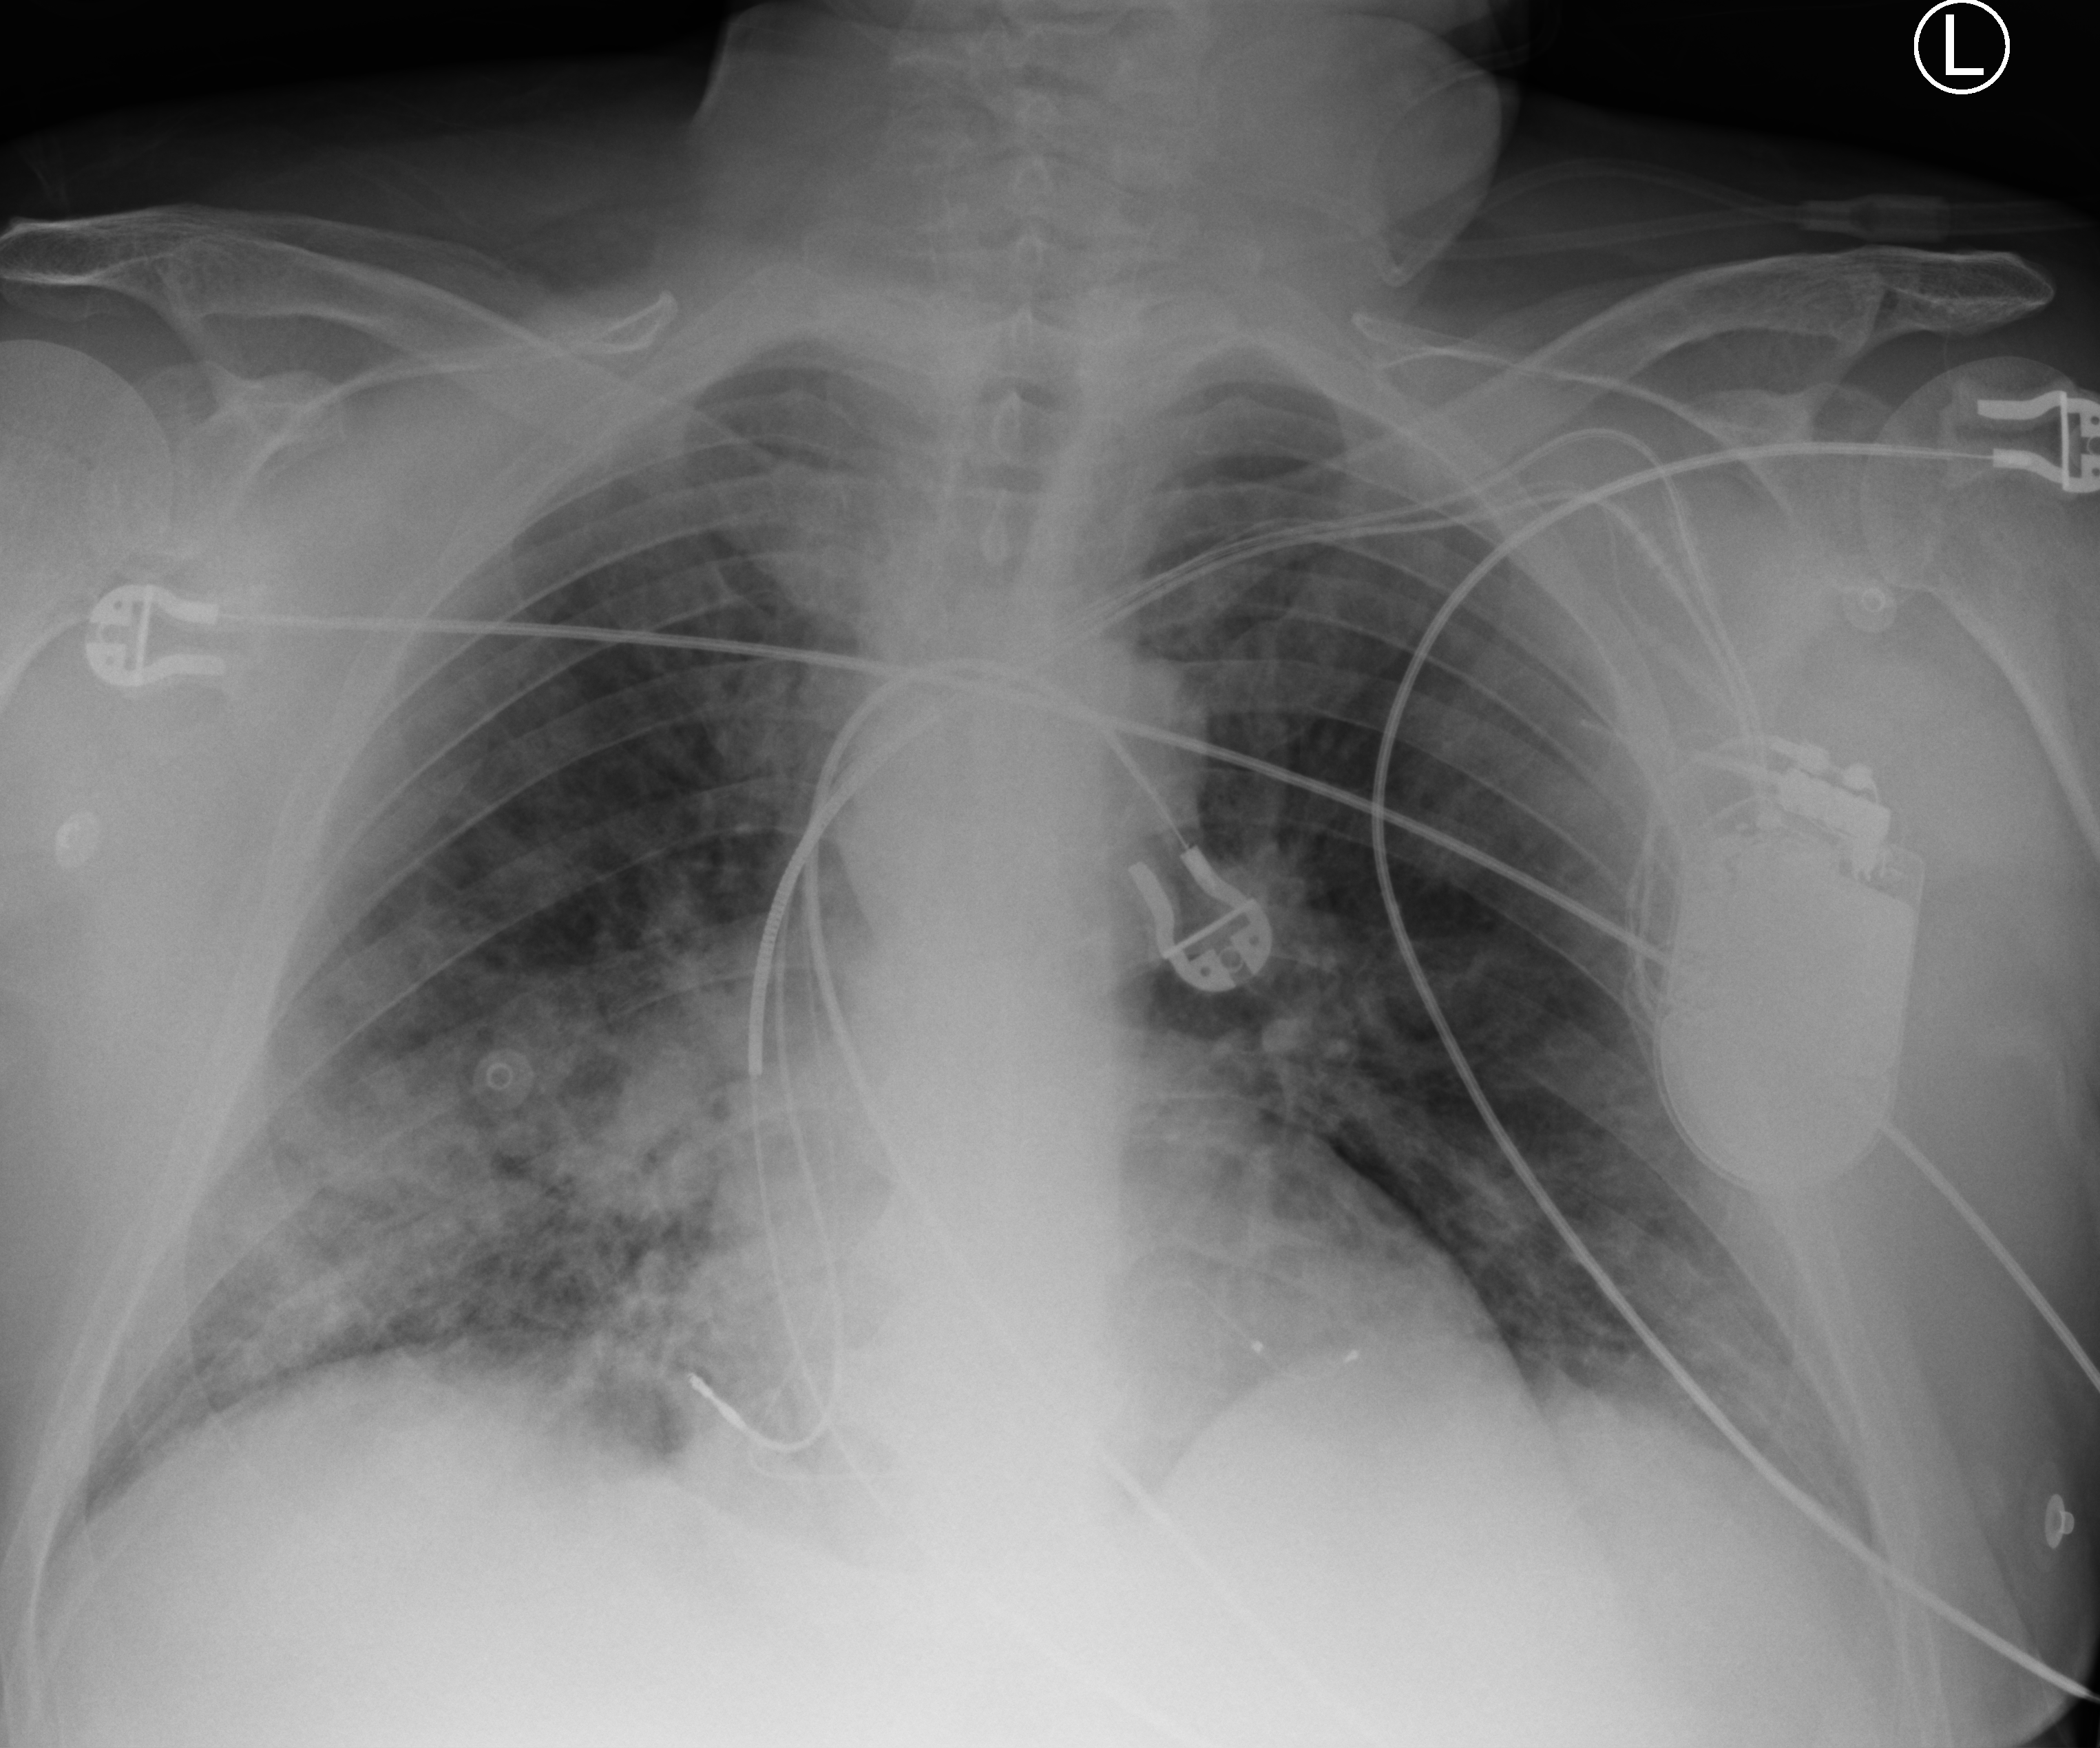
Portable chest radiograph, anteroposterior (AP) projection. Male patient hospitalised with COVID-19, age 60–74 years.
Admission-level facts for this patient (not findings on this image; timing relative to this image not recorded):
- chronic kidney disease (admission record): no
- admitted to intensive care during this hospital stay: no
- mechanically ventilated during this hospital stay: no